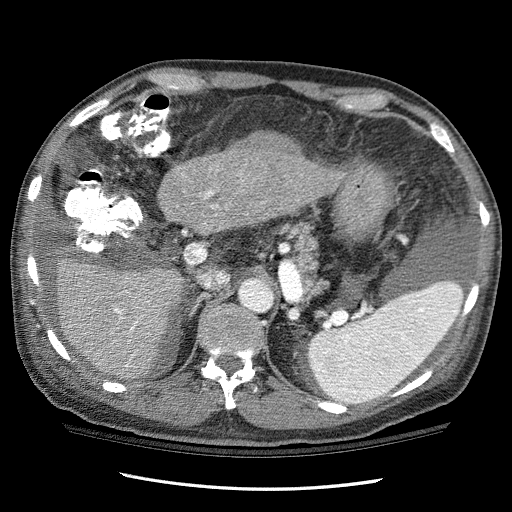
Contrast-enhanced abdominal CT (liver protocol), one axial slice. 120 kVp. One of 3 acquisitions stored at this slice position. Soft-tissue window (W 400 / L 40 HU). 2.5 mm slice thickness. 512 × 512 image matrix, field of view 360 × 360 mm. From the clinical record (not read from this slice): diagnosis: hepatocellular carcinoma (patient treated with transarterial chemoembolisation; whether this scan precedes or follows treatment is not stated here); TNM stage (as recorded): Stage-I; Child-Pugh class: C.
Structures marked on this image (semi-automatically segmented with operator editing):
- liver parenchyma outside the tumour (the mass and vessels are separate outlines, so this box may not span the whole liver): bounding box <43,129,344,380> (left, top, right, bottom; pixels)
- mass: <229,132,305,185>
- liver vessels: <115,191,218,367>